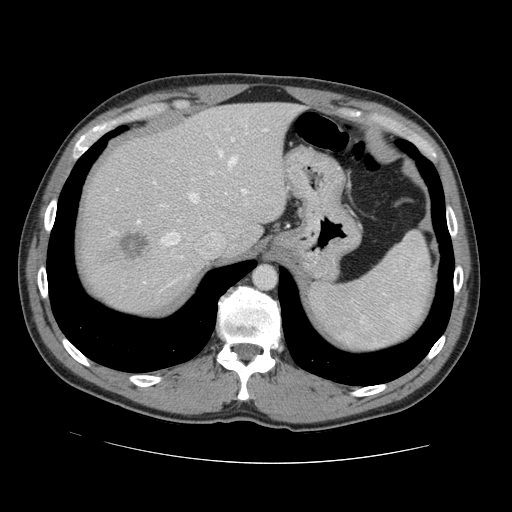
Contrast-enhanced abdominal CT, one axial slice; 120 kVp; intravenous contrast given; soft-tissue window (W 400 / L 40 HU); 512 × 512 image matrix. Male patient, age 40 years. From the clinical record (not read from this slice): diagnosis: colorectal cancer liver metastases, imaged before liver resection; multiple liver metastases: yes; largest metastasis: 2.9 cm; chemotherapy before resection: yes.
Annotated regions visible in this slice (manually delineated by an expert):
- hepatic veins: bounding box (x1, y1, x2, y2) in pixels: (161, 151, 237, 246)
- liver: (77, 104, 296, 312)
- planned liver remnant (the part of the liver to remain after resection): (105, 104, 298, 254)
- portal vein (with intrahepatic branches): (210, 133, 248, 194)
- liver metastasis: (119, 229, 150, 265)